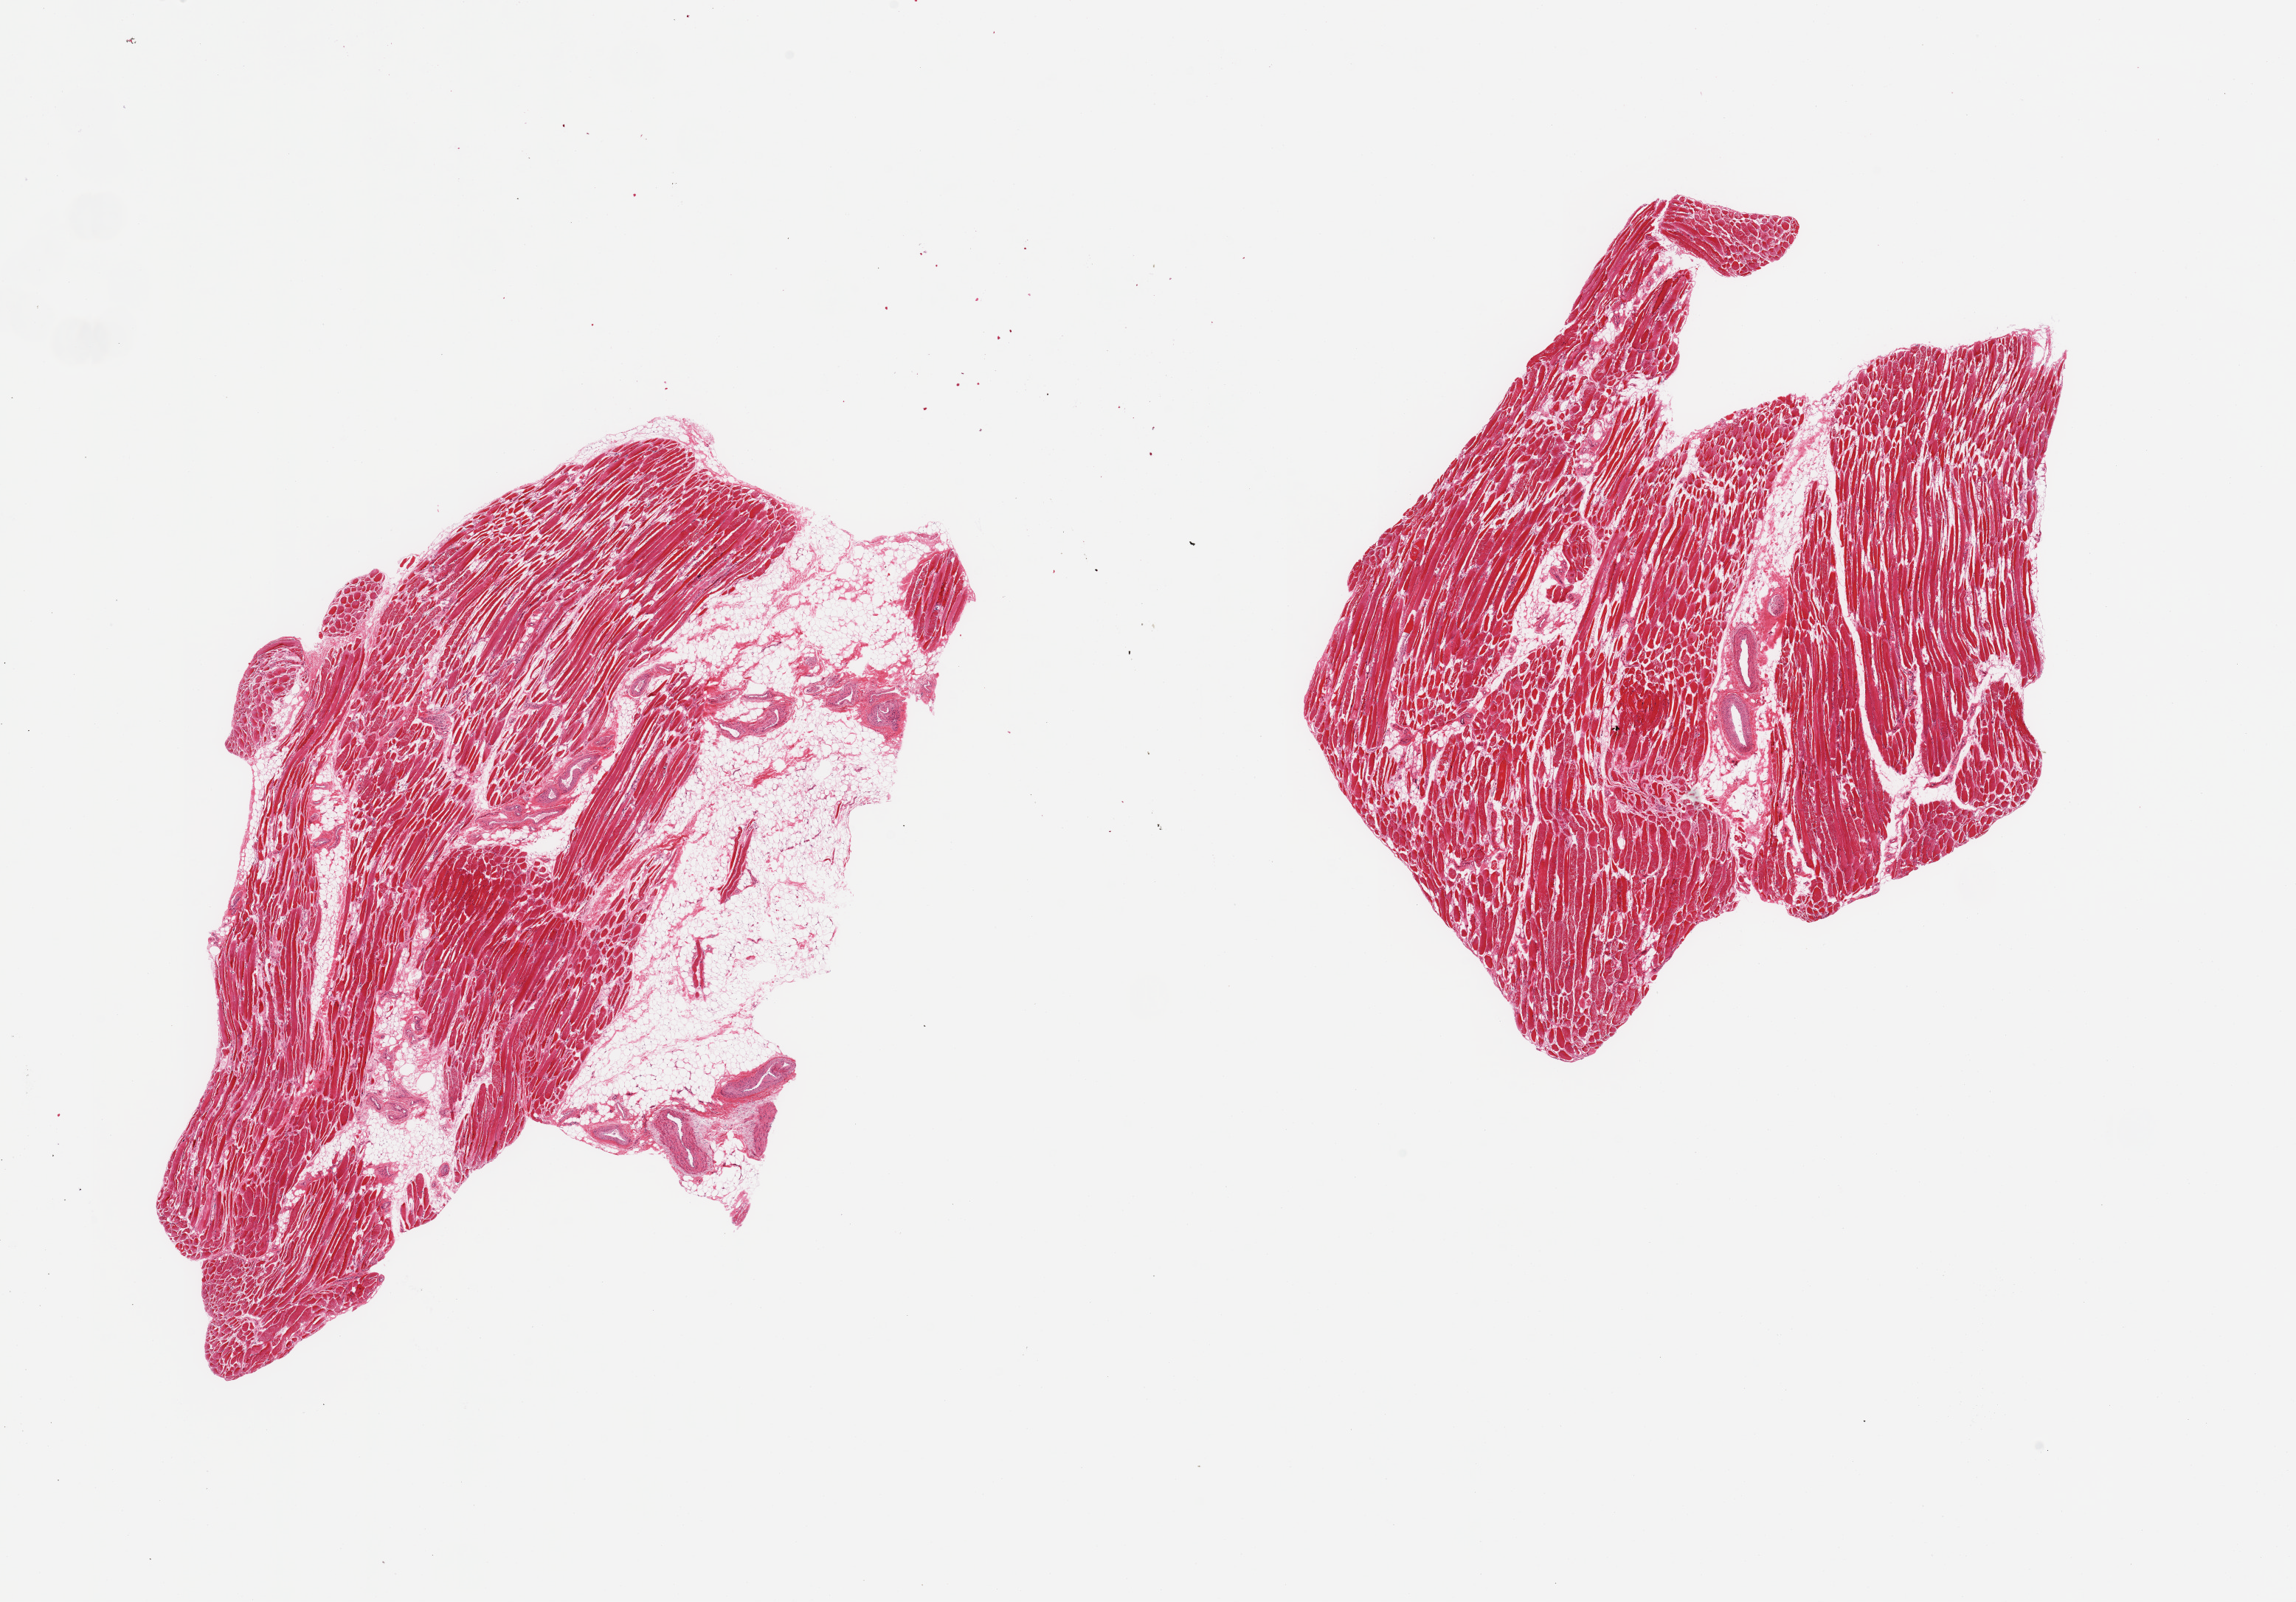
Digitized H&E-stained section, brightfield, low-resolution overview of the scanned area, about 24.6 x 17.2 mm (from a 20x scan). PAXgene-fixed paraffin-embedded (PFPE) section. Section of skeletal muscle (target tissue). Donor tissue sample. Donor: male.
Pathologist's review note for this sample: 2 pieces; scattered atrophic fibers; 20% mostly external fat.